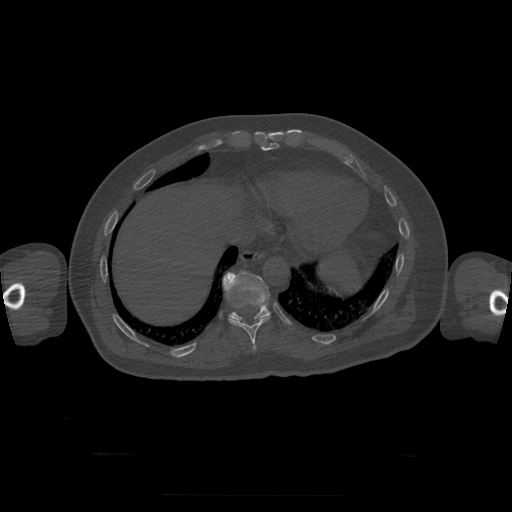
CT including the spine, one axial slice. Position 114 of 397 along the scan axis. Reconstruction kernel STANDARD. 120 kVp. Bone window (W 1800 / L 400 HU). 512 × 512 image matrix, field of view 510 × 510 mm. Patient age 73 years. From the clinical record (not read from this slice): primary cancer: prostate.
Outlined on this slice (semi-automatically segmented with operator editing):
- T10 vertebra: box from (x=228, y=316) to (x=271, y=351) px
- T11 vertebra: (x=223, y=271)–(x=271, y=323)